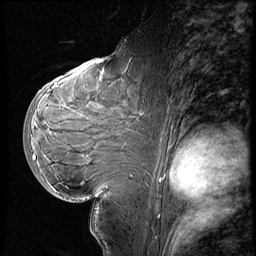
Breast MRI (dynamic contrast-enhanced), one sagittal slice. Slice 34 of 60 in the series (ordered by position). 3 images stored at this slice position (order not interpretable as contrast timing). 1.5 T. TE 4.2 ms, TR 8.9 ms. 2.5 mm slice thickness. 256 × 256 image matrix. Female patient, age 29 years. From the clinical record (not read from this slice): setting: breast cancer imaged before/during neoadjuvant chemotherapy.
Outlined on this slice (semi-automatic segmentation, software-assisted and operator-edited):
- analysis volume of interest (the breast-tissue region the enhancement analysis was run in; not a lesion): bounding box [x1, y1, x2, y2] px = [29, 57, 150, 200]
- tumour enhancement mask (voxels above the 140 % enhancement threshold inside the analysis volume of interest): [35, 84, 58, 160]